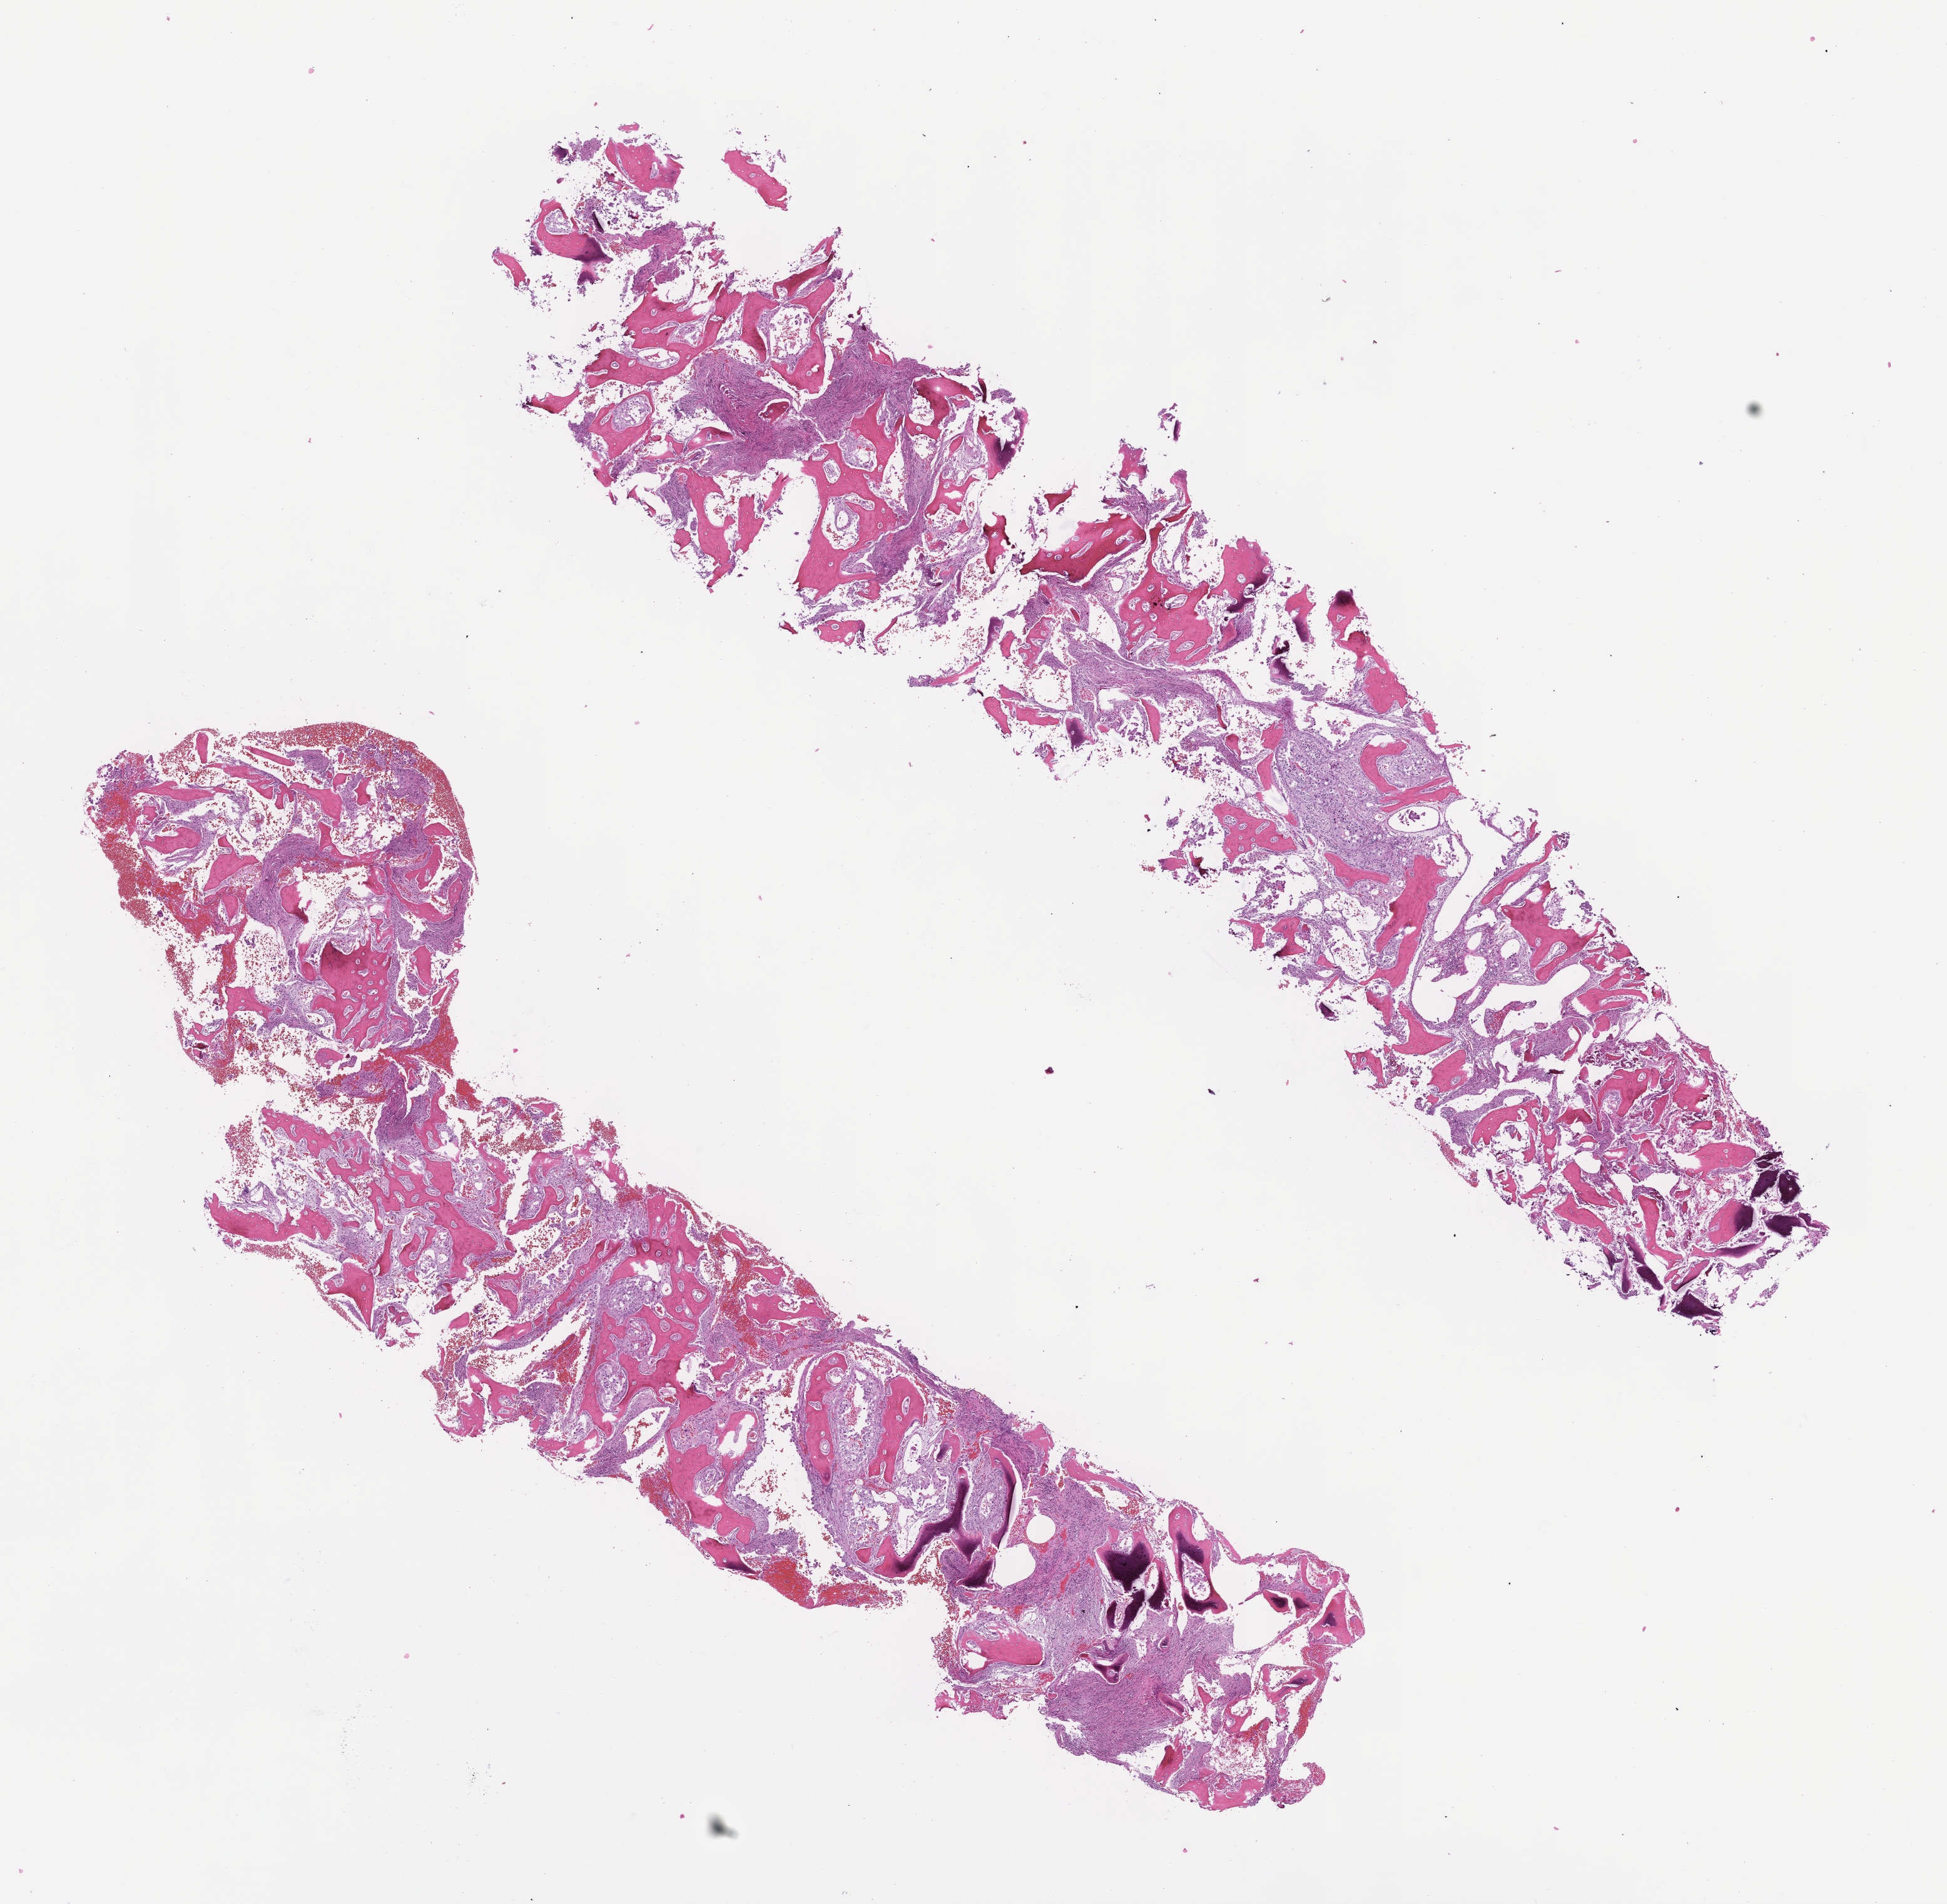
Hematoxylin and eosin (H&E) whole-slide image, low-resolution overview of the scanned area, about 12.6 x 12.3 mm, formalin-fixed, paraffin-embedded (FFPE) tissue, archival tissue. Patient sex: male.
This section: metastasis (sampled organ not recorded). Patient diagnosis (primary): Non-Small Cell Lung Carcinoma.